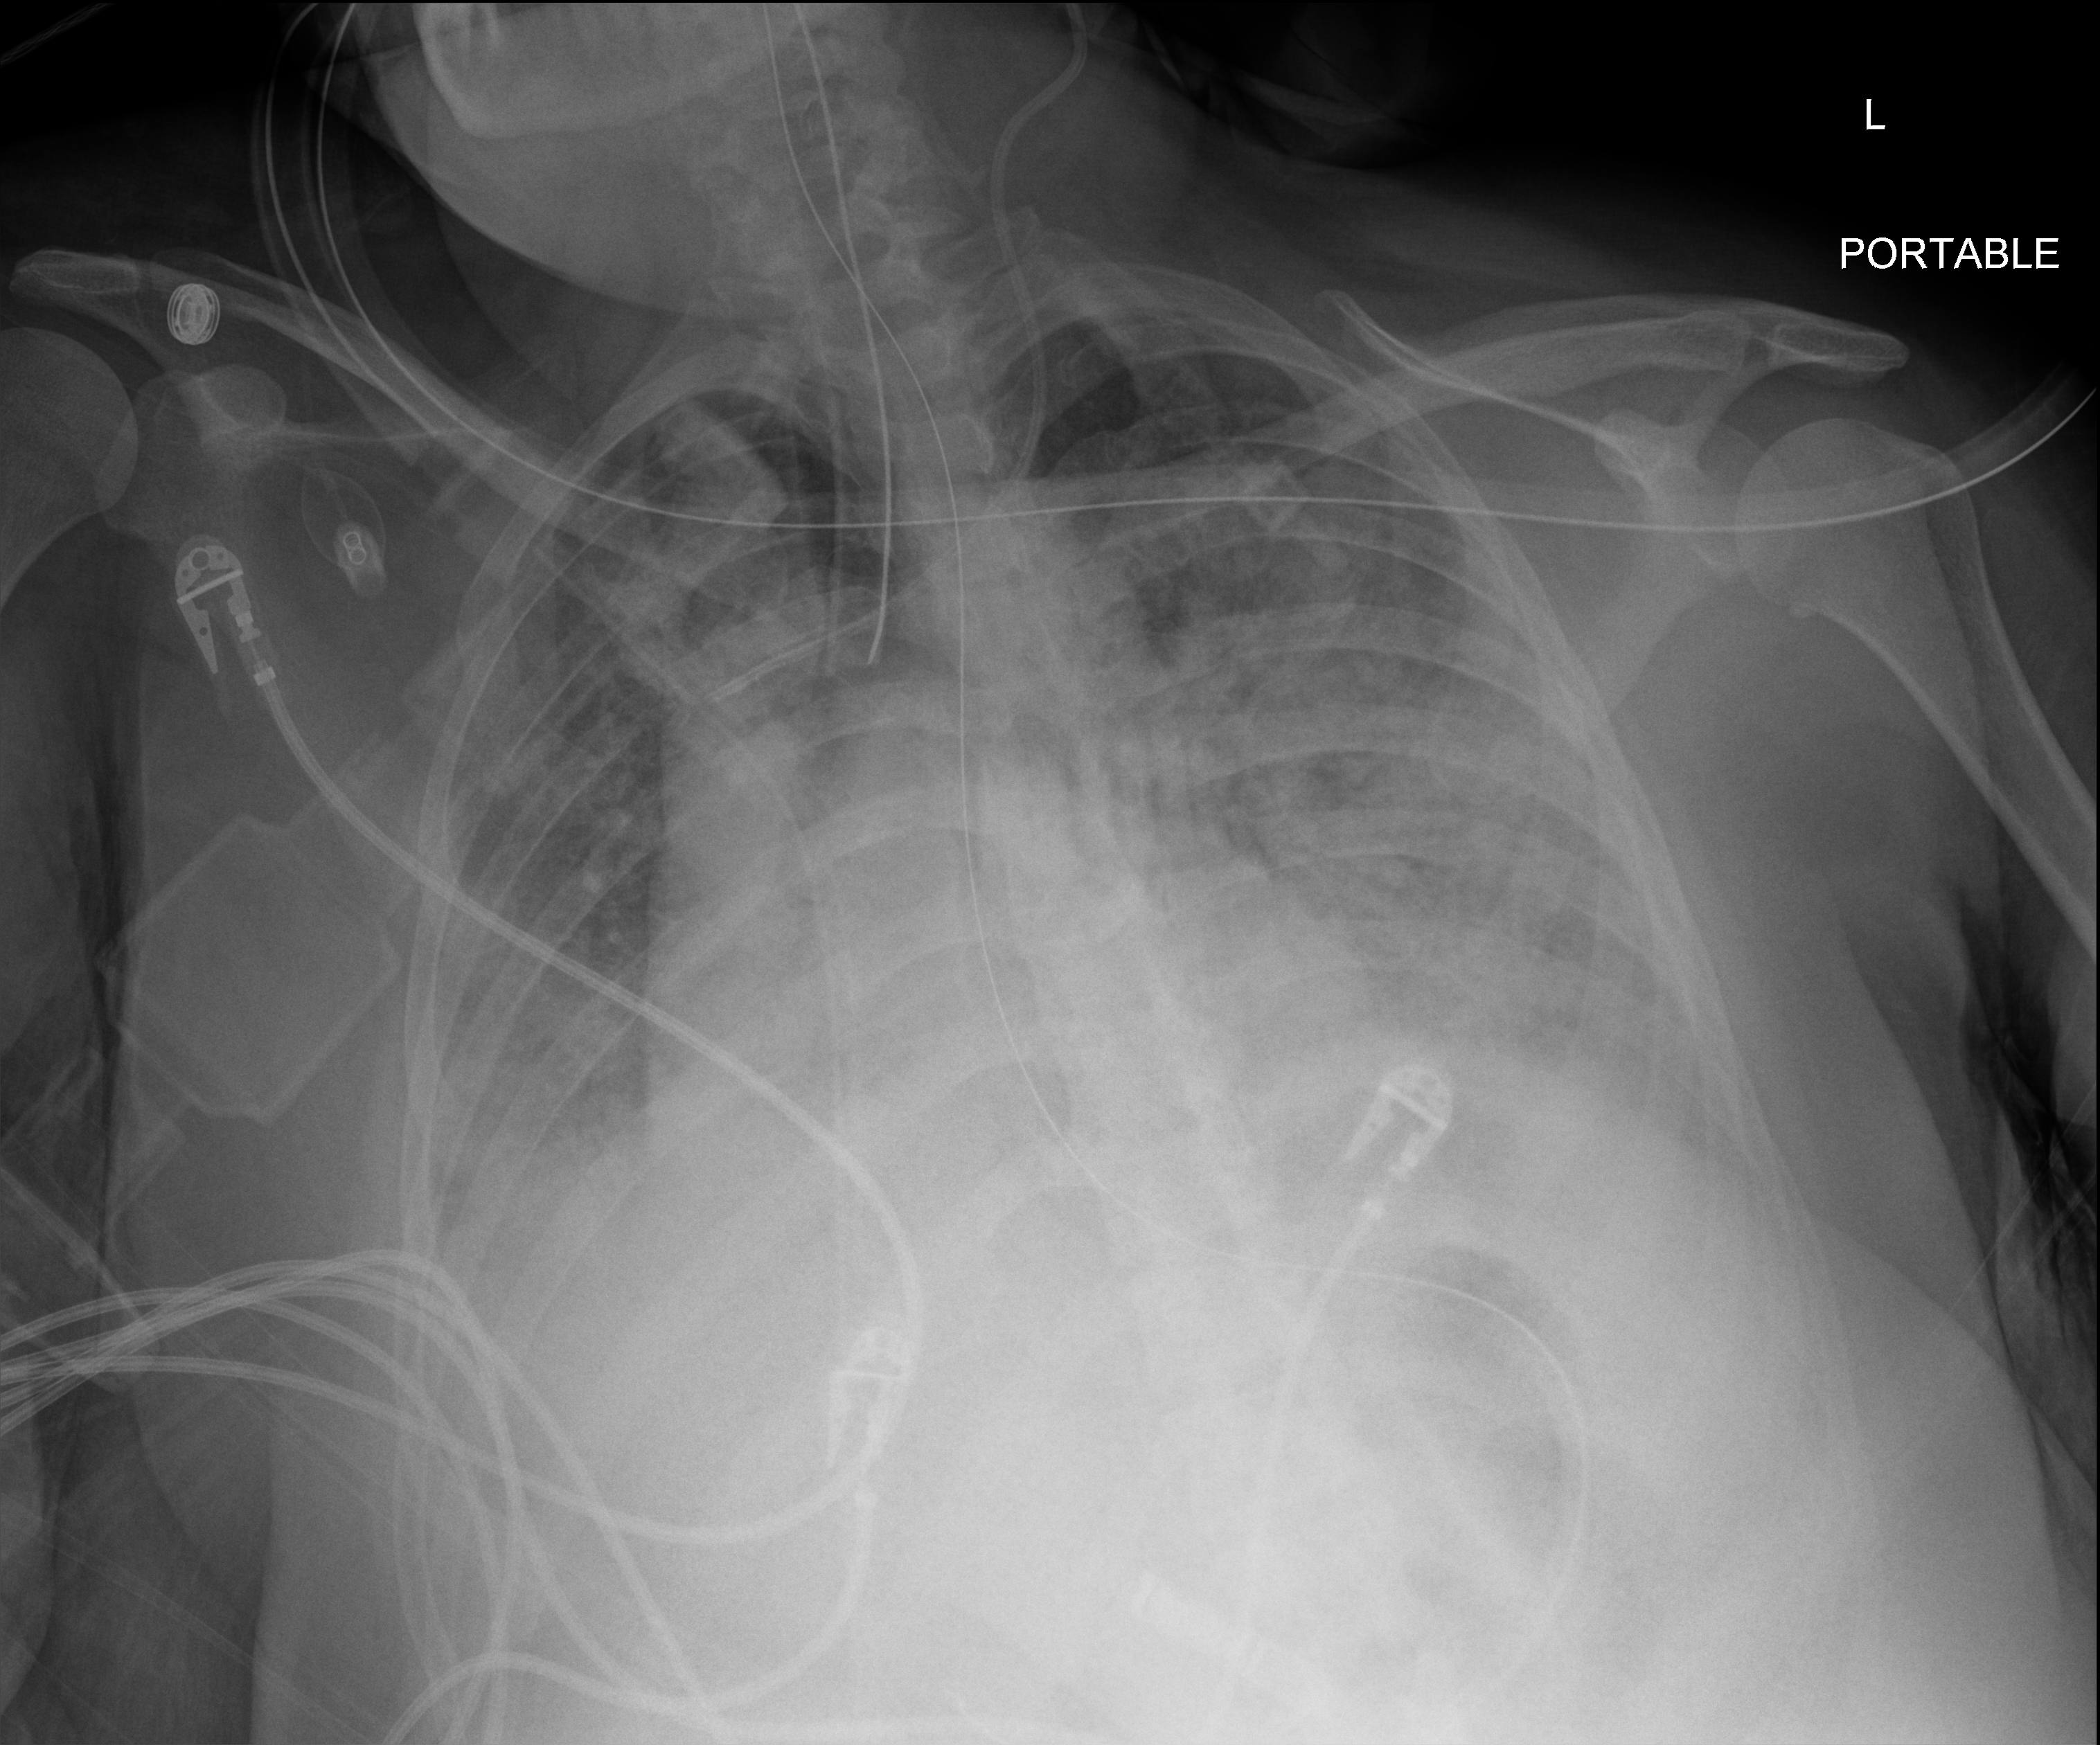
Chest X-ray (portable); anteroposterior (AP) projection. Patient hospitalised with COVID-19; female, aged 18–59 years.
From the hospital-stay record, not from the radiograph (when in the stay this image was taken is not recorded): mechanically ventilated during this hospital stay: yes.